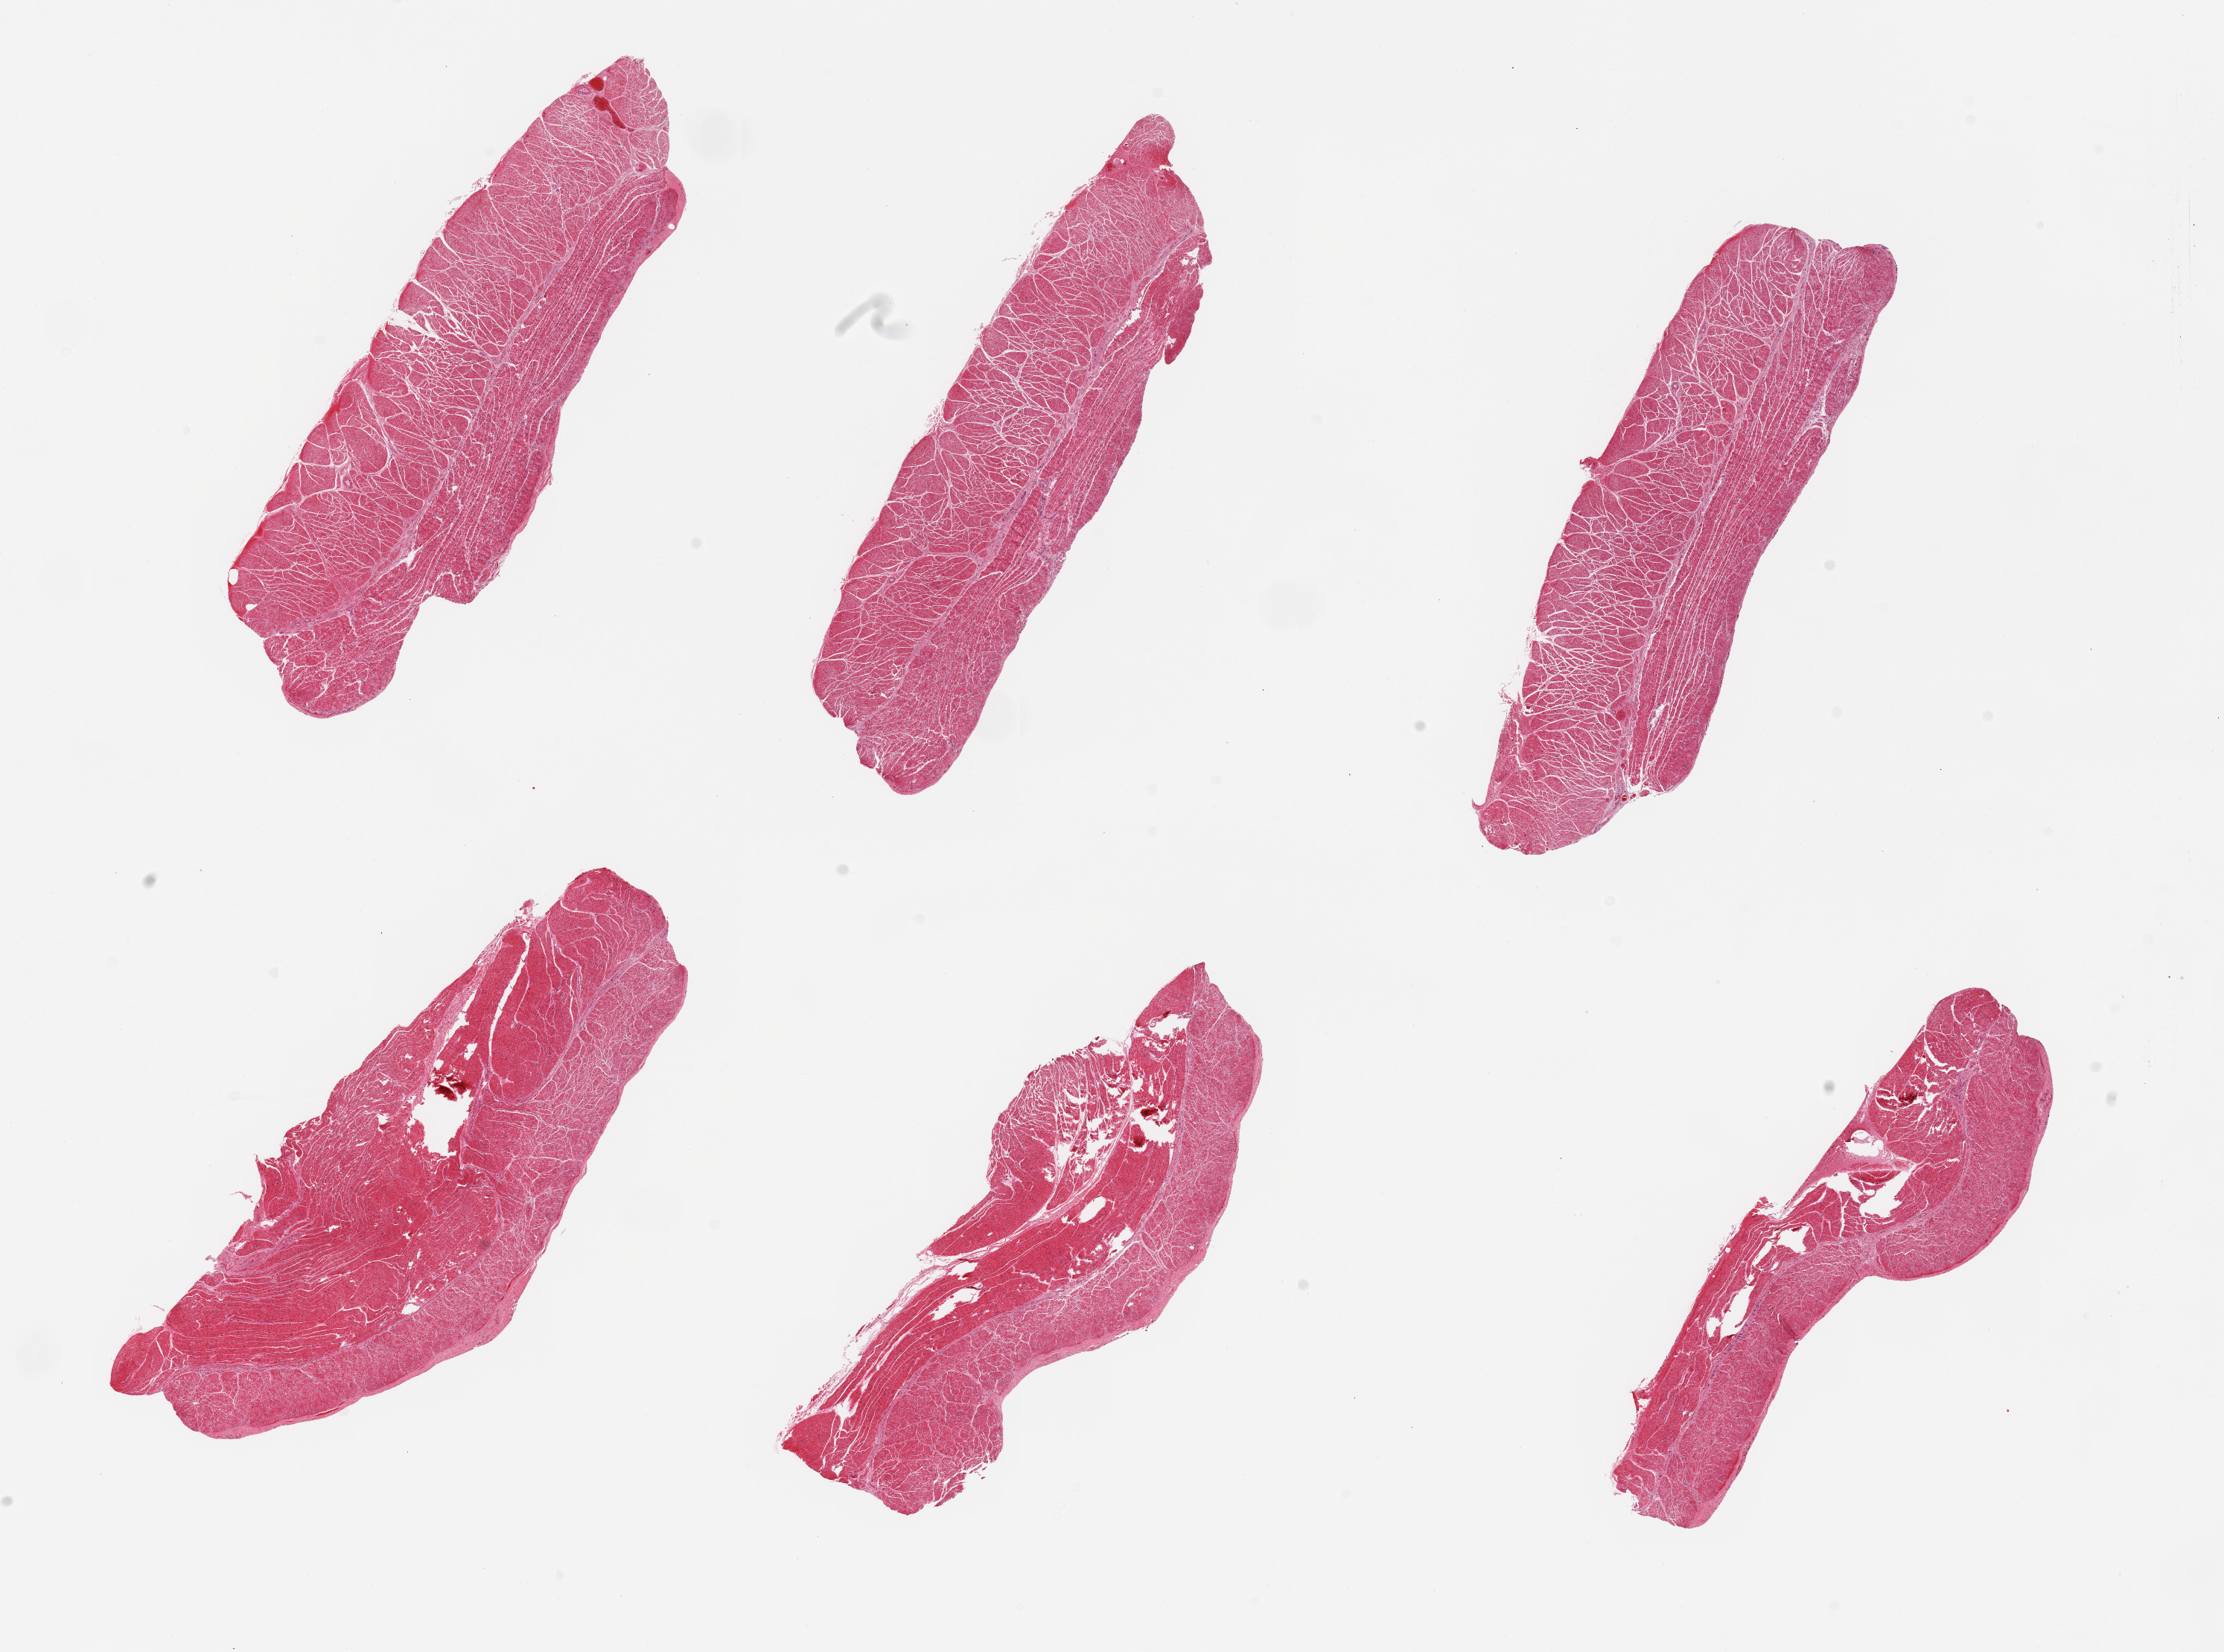
Hematoxylin and eosin (H&E) whole-slide image, brightfield, low-resolution overview of the scanned area, about 23.6 x 17.6 mm; PAXgene-fixed paraffin-embedded (PFPE) section; target tissue: esophageal muscle; tissue donor sample. Donor: female.
• review note (as recorded): 6 pieces; well trimmed